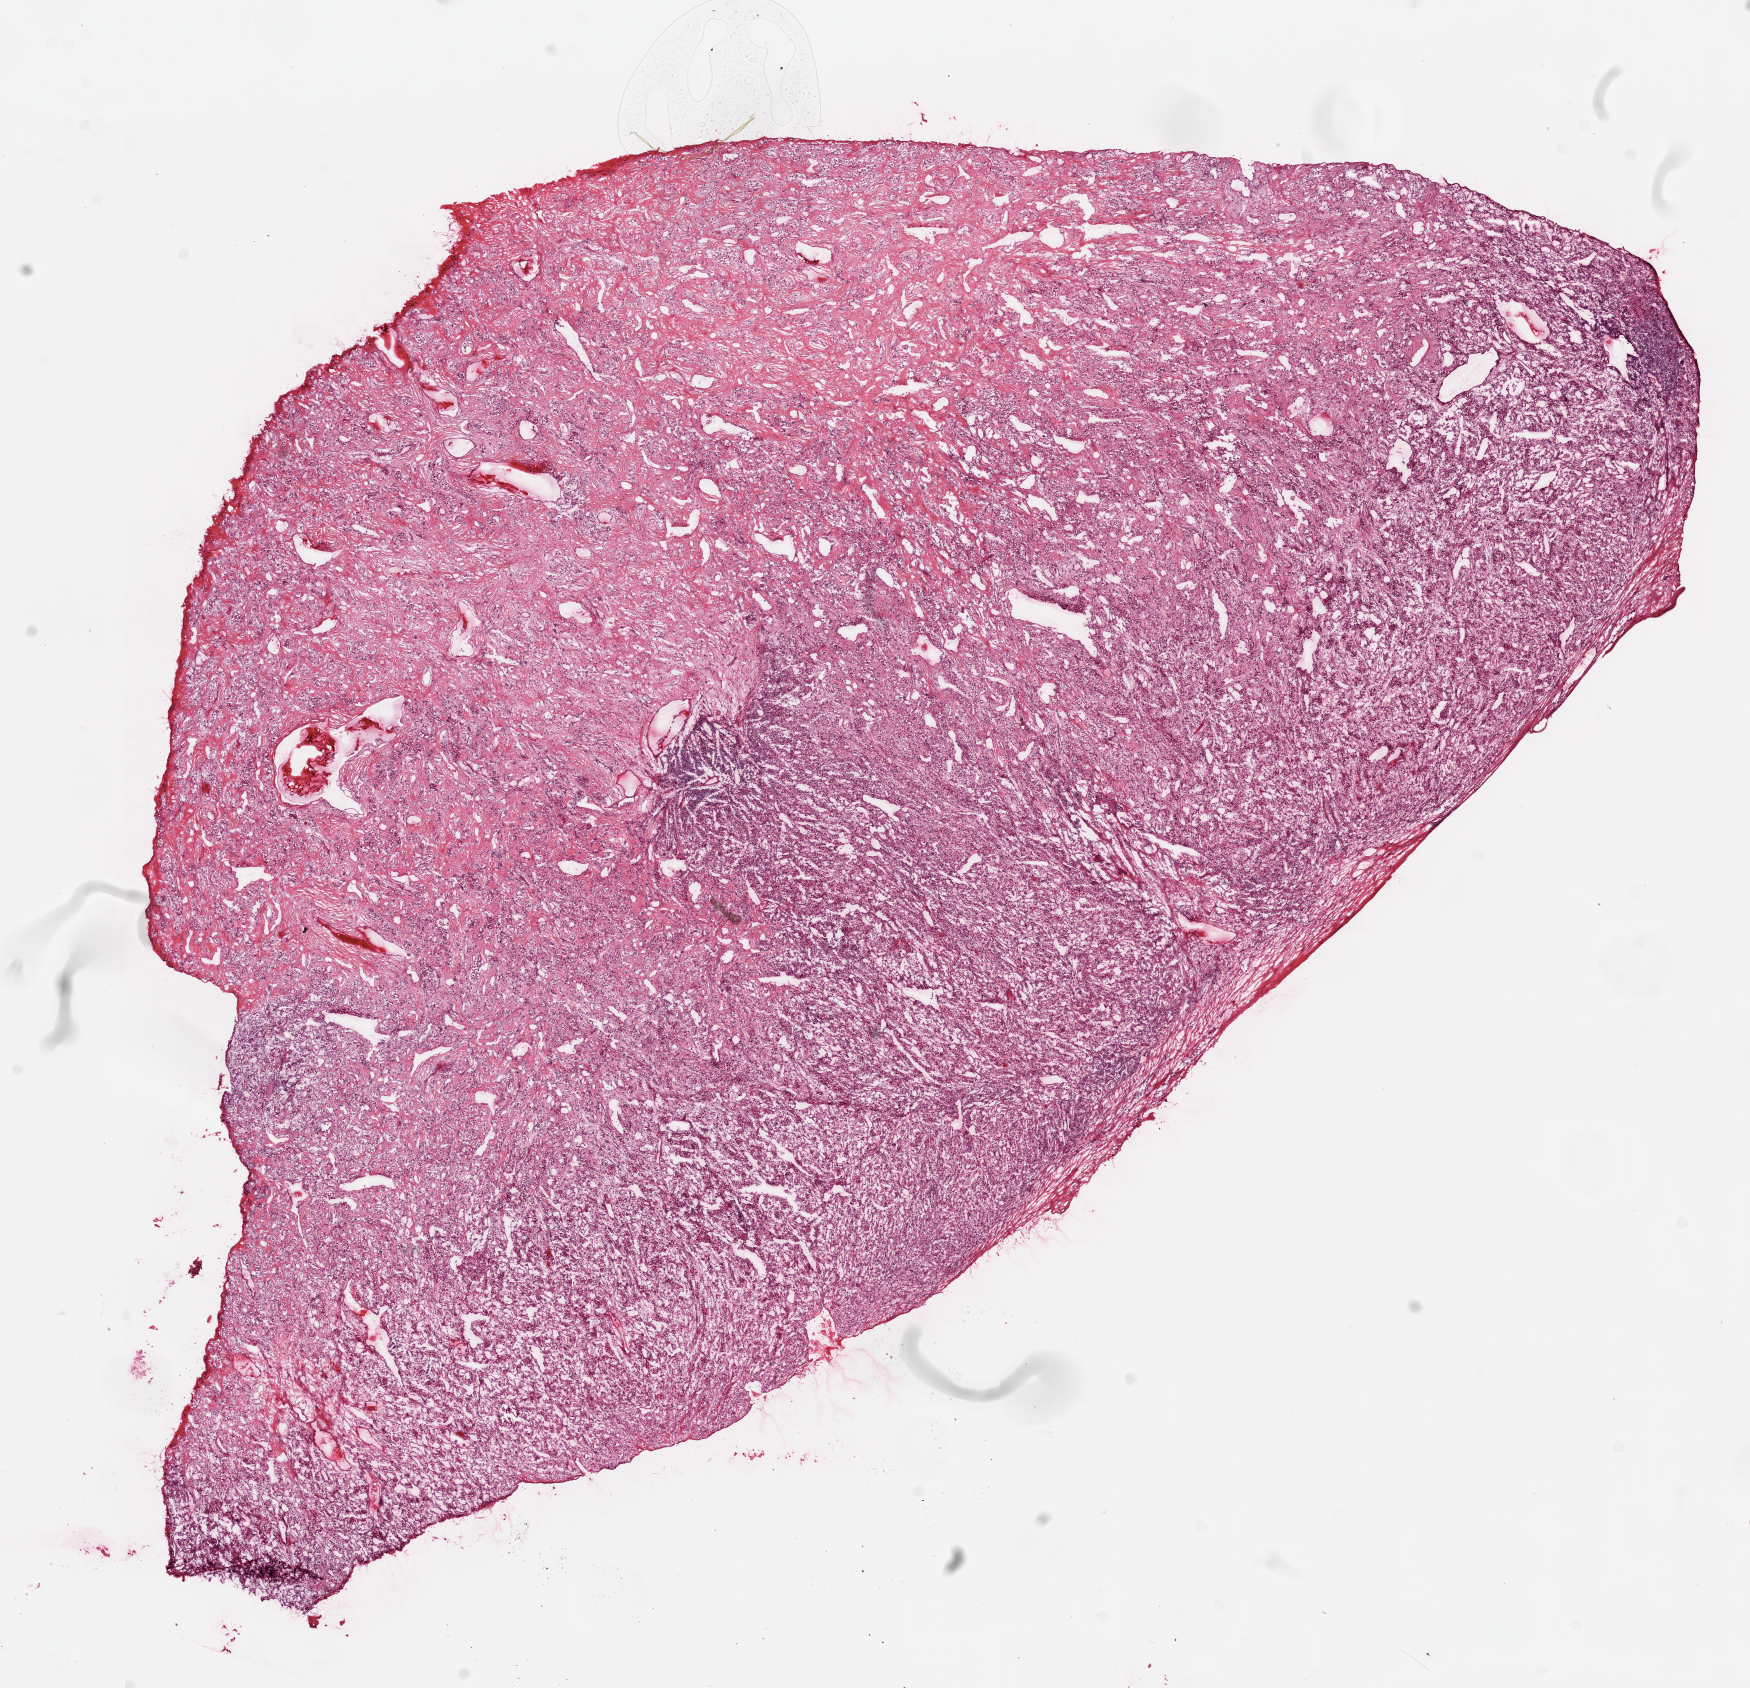
Digitized H&E-stained tissue section (whole slide) — a low-resolution overview of the entire scanned area, about 14.0 x 13.5 mm (from a 20x scan), frozen section from the top of the tissue portion, sample: primary tumour, kidney. Patient: male, age at initial diagnosis 69 years. Histologic grade: G2 (moderately differentiated). Pathologist review of this section (percent, as recorded): tumour cells 70%, tumour nuclei 80%, normal cells 0%, stromal cells 30%, necrosis 0%.
Diagnosis: Clear cell adenocarcinoma, NOS. AJCC pathologic stage: IV (6th edition). Laterality: left.